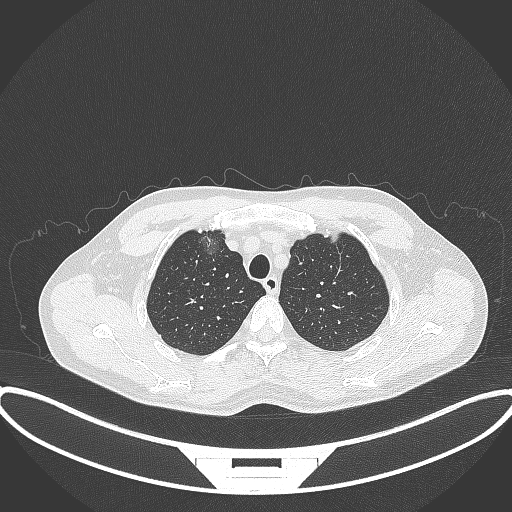
Chest CT, one axial slice. Position 302 of 395 along the scan axis. Lung window (W 1500 / L -600 HU). 1 mm slice thickness. 512 × 512 image matrix. Patient: male, 60 years. Case-level facts recorded for this patient, not image findings: clinical TNM (as recorded): T1c N0 M0.
Outlined on this slice (rectangle marked by the reading radiologist):
- lung tumour (recorded histology: adenocarcinoma): bounding box <196,226,222,260> (left, top, right, bottom; pixels)